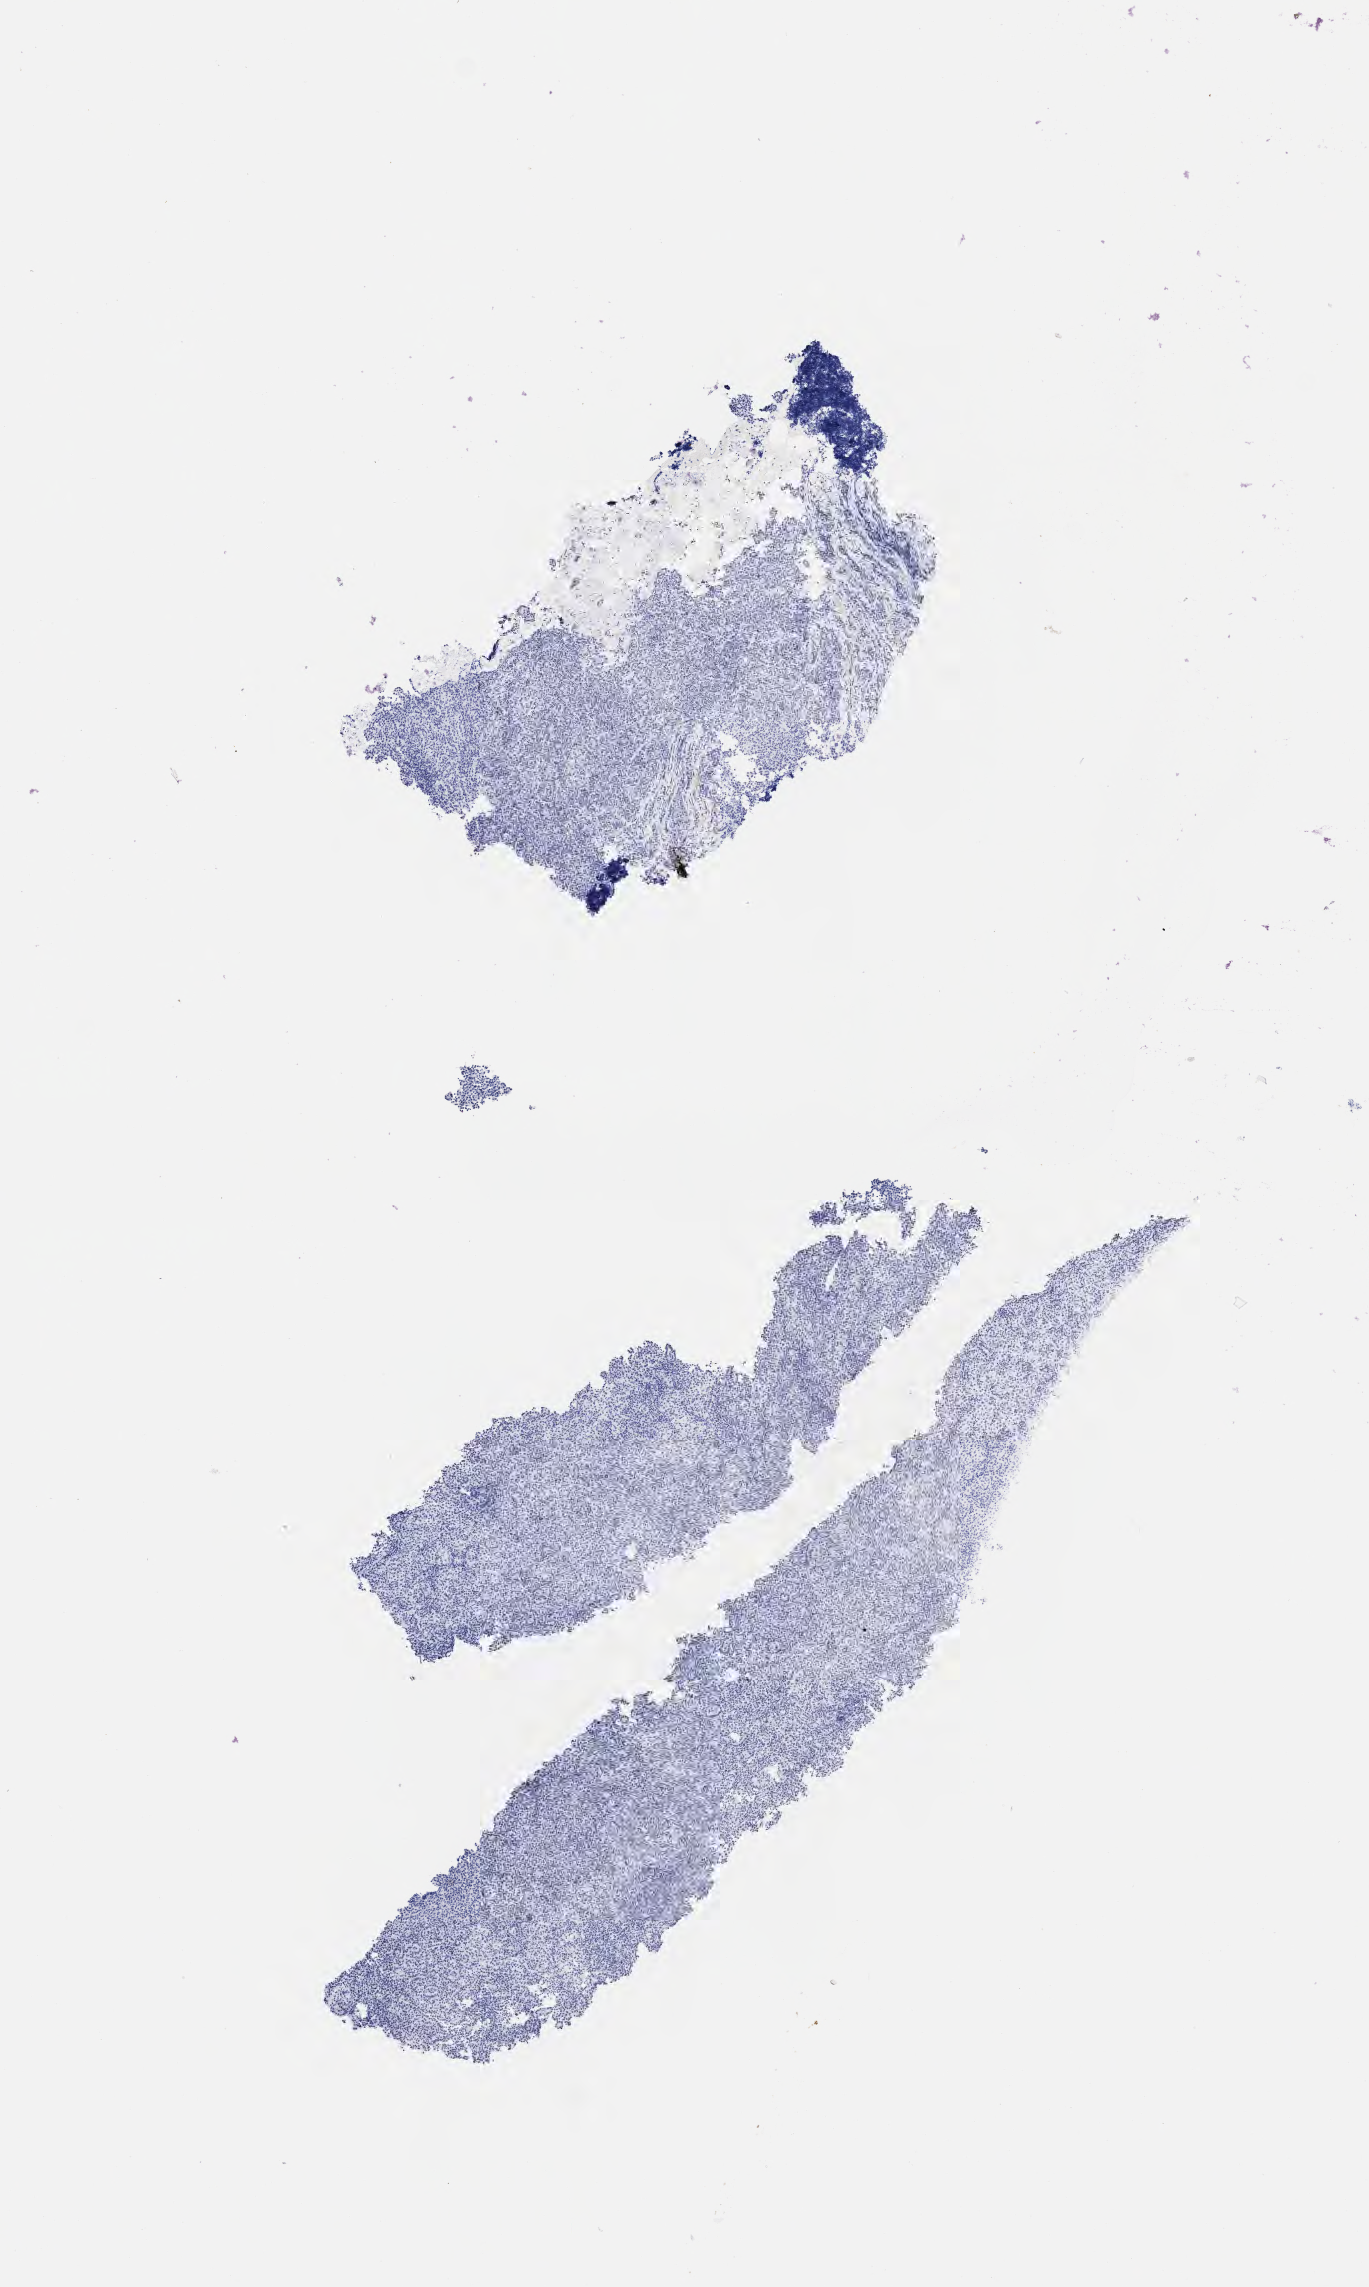
IHC for TTF-1 (thyroid transcription factor 1), whole-slide image, a low-resolution overview of the entire scanned area, about 5.5 x 9.2 mm. Tumor tissue. Site: lung (left). Female patient, 65 years old.
Histologic diagnosis: Non-small cell carcinoma.